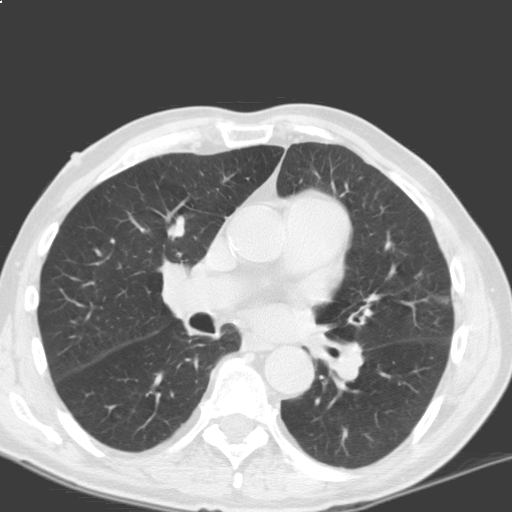
Low-dose screening chest CT, axial slice, first (baseline) screen, lung window (W 1500 / L -600 HU), 3.2 mm slice thickness, standard (soft-tissue) reconstruction kernel (C), 120 kVp, slice 86 of 184 in the series. Male, age 69 years at enrolment. Current smoker at enrolment.
- Expert reader's lesion annotation, bounding box [x1, y1, x2, y2] px = [147, 205, 207, 254].
- The exam's reader record, not a measurement of the box and not confirmed to be the same lesion: non-calcified nodule or mass ≥4 mm, left lower lobe, 5 × 5 mm, smooth margins, soft tissue attenuation.
- Note: the box lies in the patient's right hemithorax on this image, whereas the reader's record names the left lung; they may be different findings.
- Official screen result: positive, change unspecified: nodule(s) >= 4 mm or enlarging nodule(s), mass(es), or other non-specific abnormalities suspicious for lung cancer.
- Later outcome: lung cancer diagnosed 317 days after this screen — squamous cell carcinoma, NOS, right upper lobe, moderately differentiated (G2), stage IB (AJCC 6th edition), 40 mm at pathology.